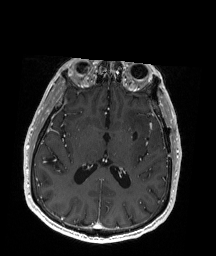
Brain MRI from a brain-tumour surgery series, one axial slice. Slice 91 of 192 in the series (ordered by position). T1-weighted post-contrast. 1 mm slice thickness. 216 × 256 image matrix. From the clinical record (not read from this slice): histopathology: Oligodendroglioma; WHO grade: 2; IDH mutation: yes.
Outlined on this slice (outlined manually by an expert reader):
- previous resection cavity: box from (x=136, y=127) to (x=158, y=138) px